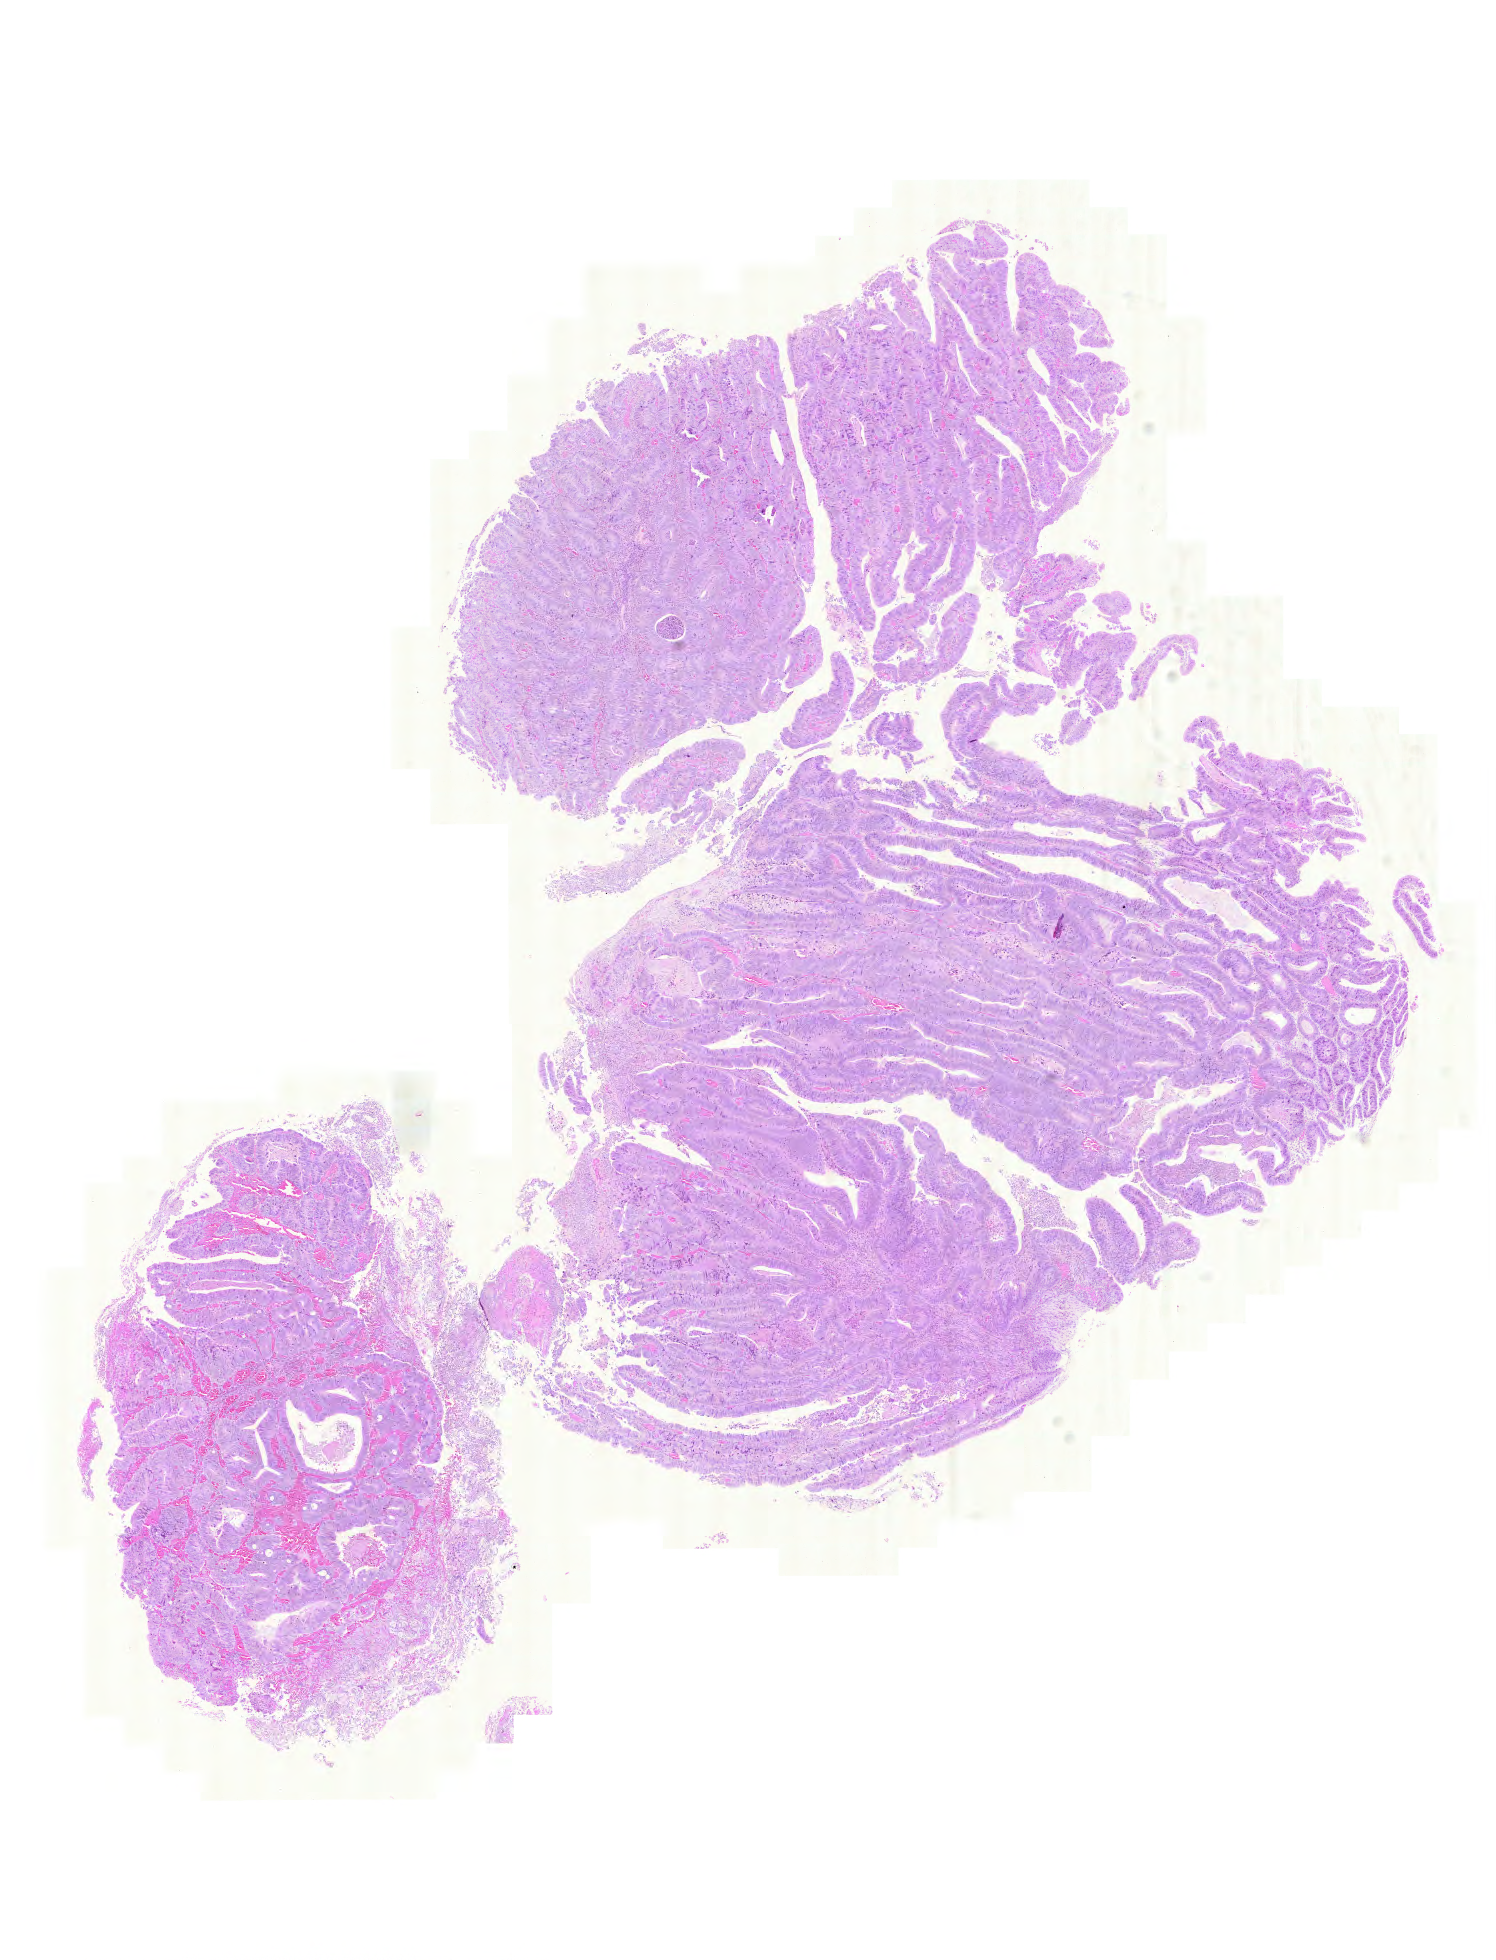
Digitized Hematoxylin and eosin (H&E) stained tissue section (whole slide) — shown as a low-resolution overview of the whole scanned area (about 11.1 x 14.6 mm), FFPE section, sample: primary tumour, stomach. Patient: male, age at initial diagnosis 57 years. Histologic grade: G2 (moderately differentiated).
* AJCC pathologic stage: IB (6th edition)
* TNM: T2 N0 M0
* pathologic diagnosis: Adenocarcinoma, intestinal type
* lymph nodes positive (case pathology): 0 of 58 examined